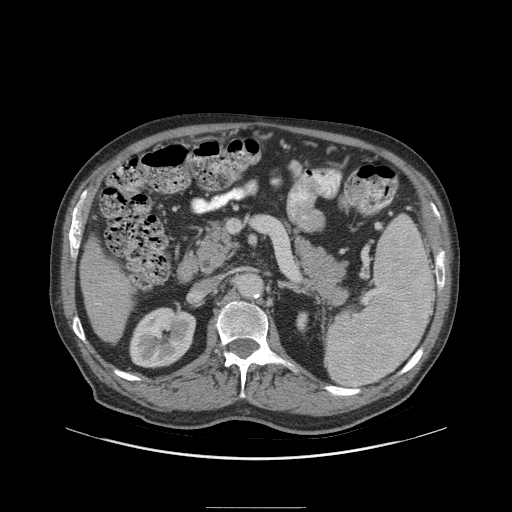
Contrast-enhanced abdominal CT (liver protocol), one axial slice. Position 36 of 105 along the scan axis. Soft-tissue window (W 400 / L 40 HU). 2.5 mm slice thickness. 512 × 512 image matrix, field of view 440 × 440 mm. From the clinical record (not read from this slice): diagnosis: hepatocellular carcinoma (patient treated with transarterial chemoembolisation; whether this scan precedes or follows treatment is not stated here); TNM stage (as recorded): Stage-I; Child-Pugh class: A; tumour nodularity: uninodular; tumour size: 5.1 cm.
Outlined on this slice (semi-automatically segmented with operator editing):
- liver parenchyma outside the tumour (the mass and vessels are separate outlines, so this box may not span the whole liver): bounding box (x1, y1, x2, y2) in pixels: (80, 236, 134, 342)